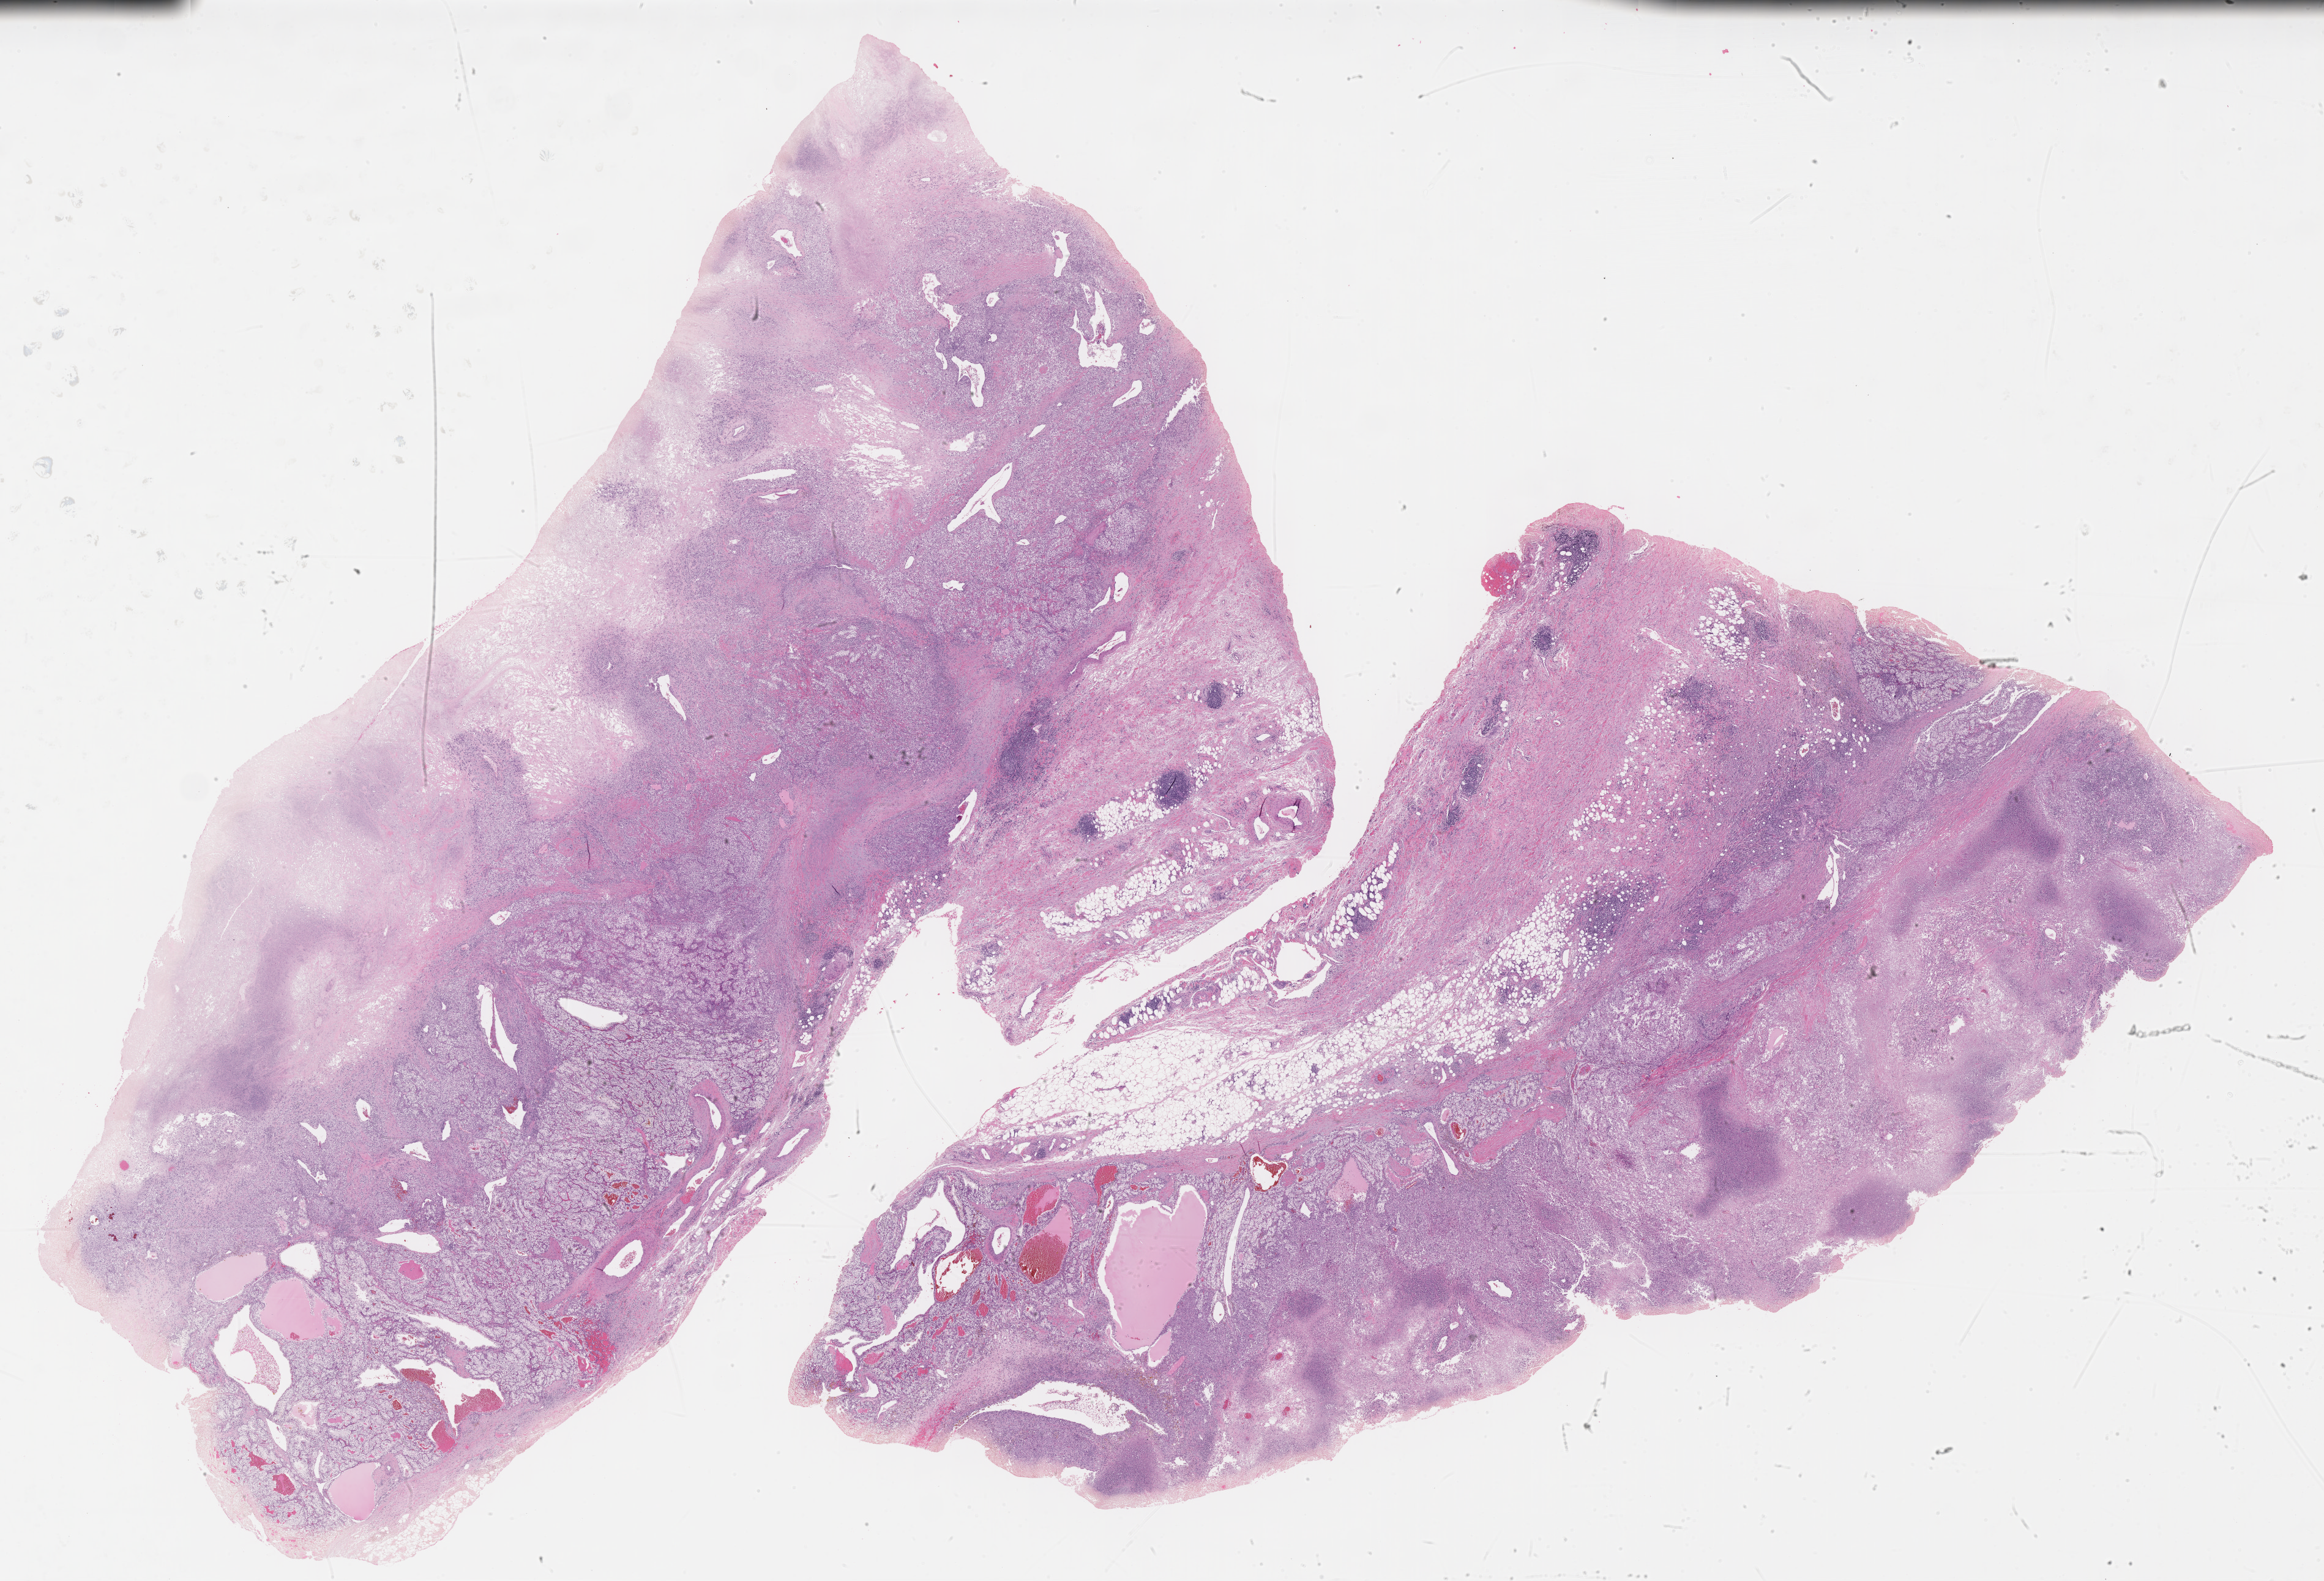
Hematoxylin and eosin (H&E) stained whole-slide image — a low-resolution overview of the entire scanned area, about 30.7 x 20.9 mm (acquisition: 40x scan), formalin-fixed paraffin-embedded (FFPE) diagnostic section, kidney, primary tumour sample. Male patient; age at initial diagnosis 42 years.
Pathologic diagnosis: Clear cell adenocarcinoma, NOS.